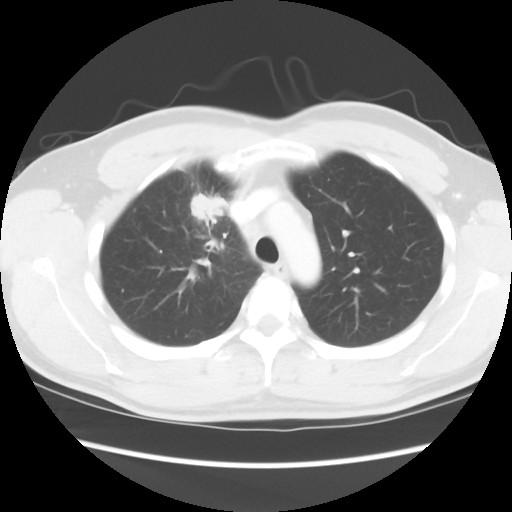
Chest CT, one axial slice; slice 66 of 80 in the series (ordered by position); reconstruction kernel STANDARD; lung window (W 1500 / L -600 HU); 5 mm slice thickness; 512 × 512 image matrix, field of view 360 × 360 mm. Male patient, age 35 years. From the clinical record (not read from this slice): clinical TNM (as recorded): T1c N1 M1b.
Outlined on this slice (rectangle marked by the reading radiologist):
- lung tumour (recorded histology: adenocarcinoma): bounding box [x1, y1, x2, y2] px = [188, 186, 228, 227]